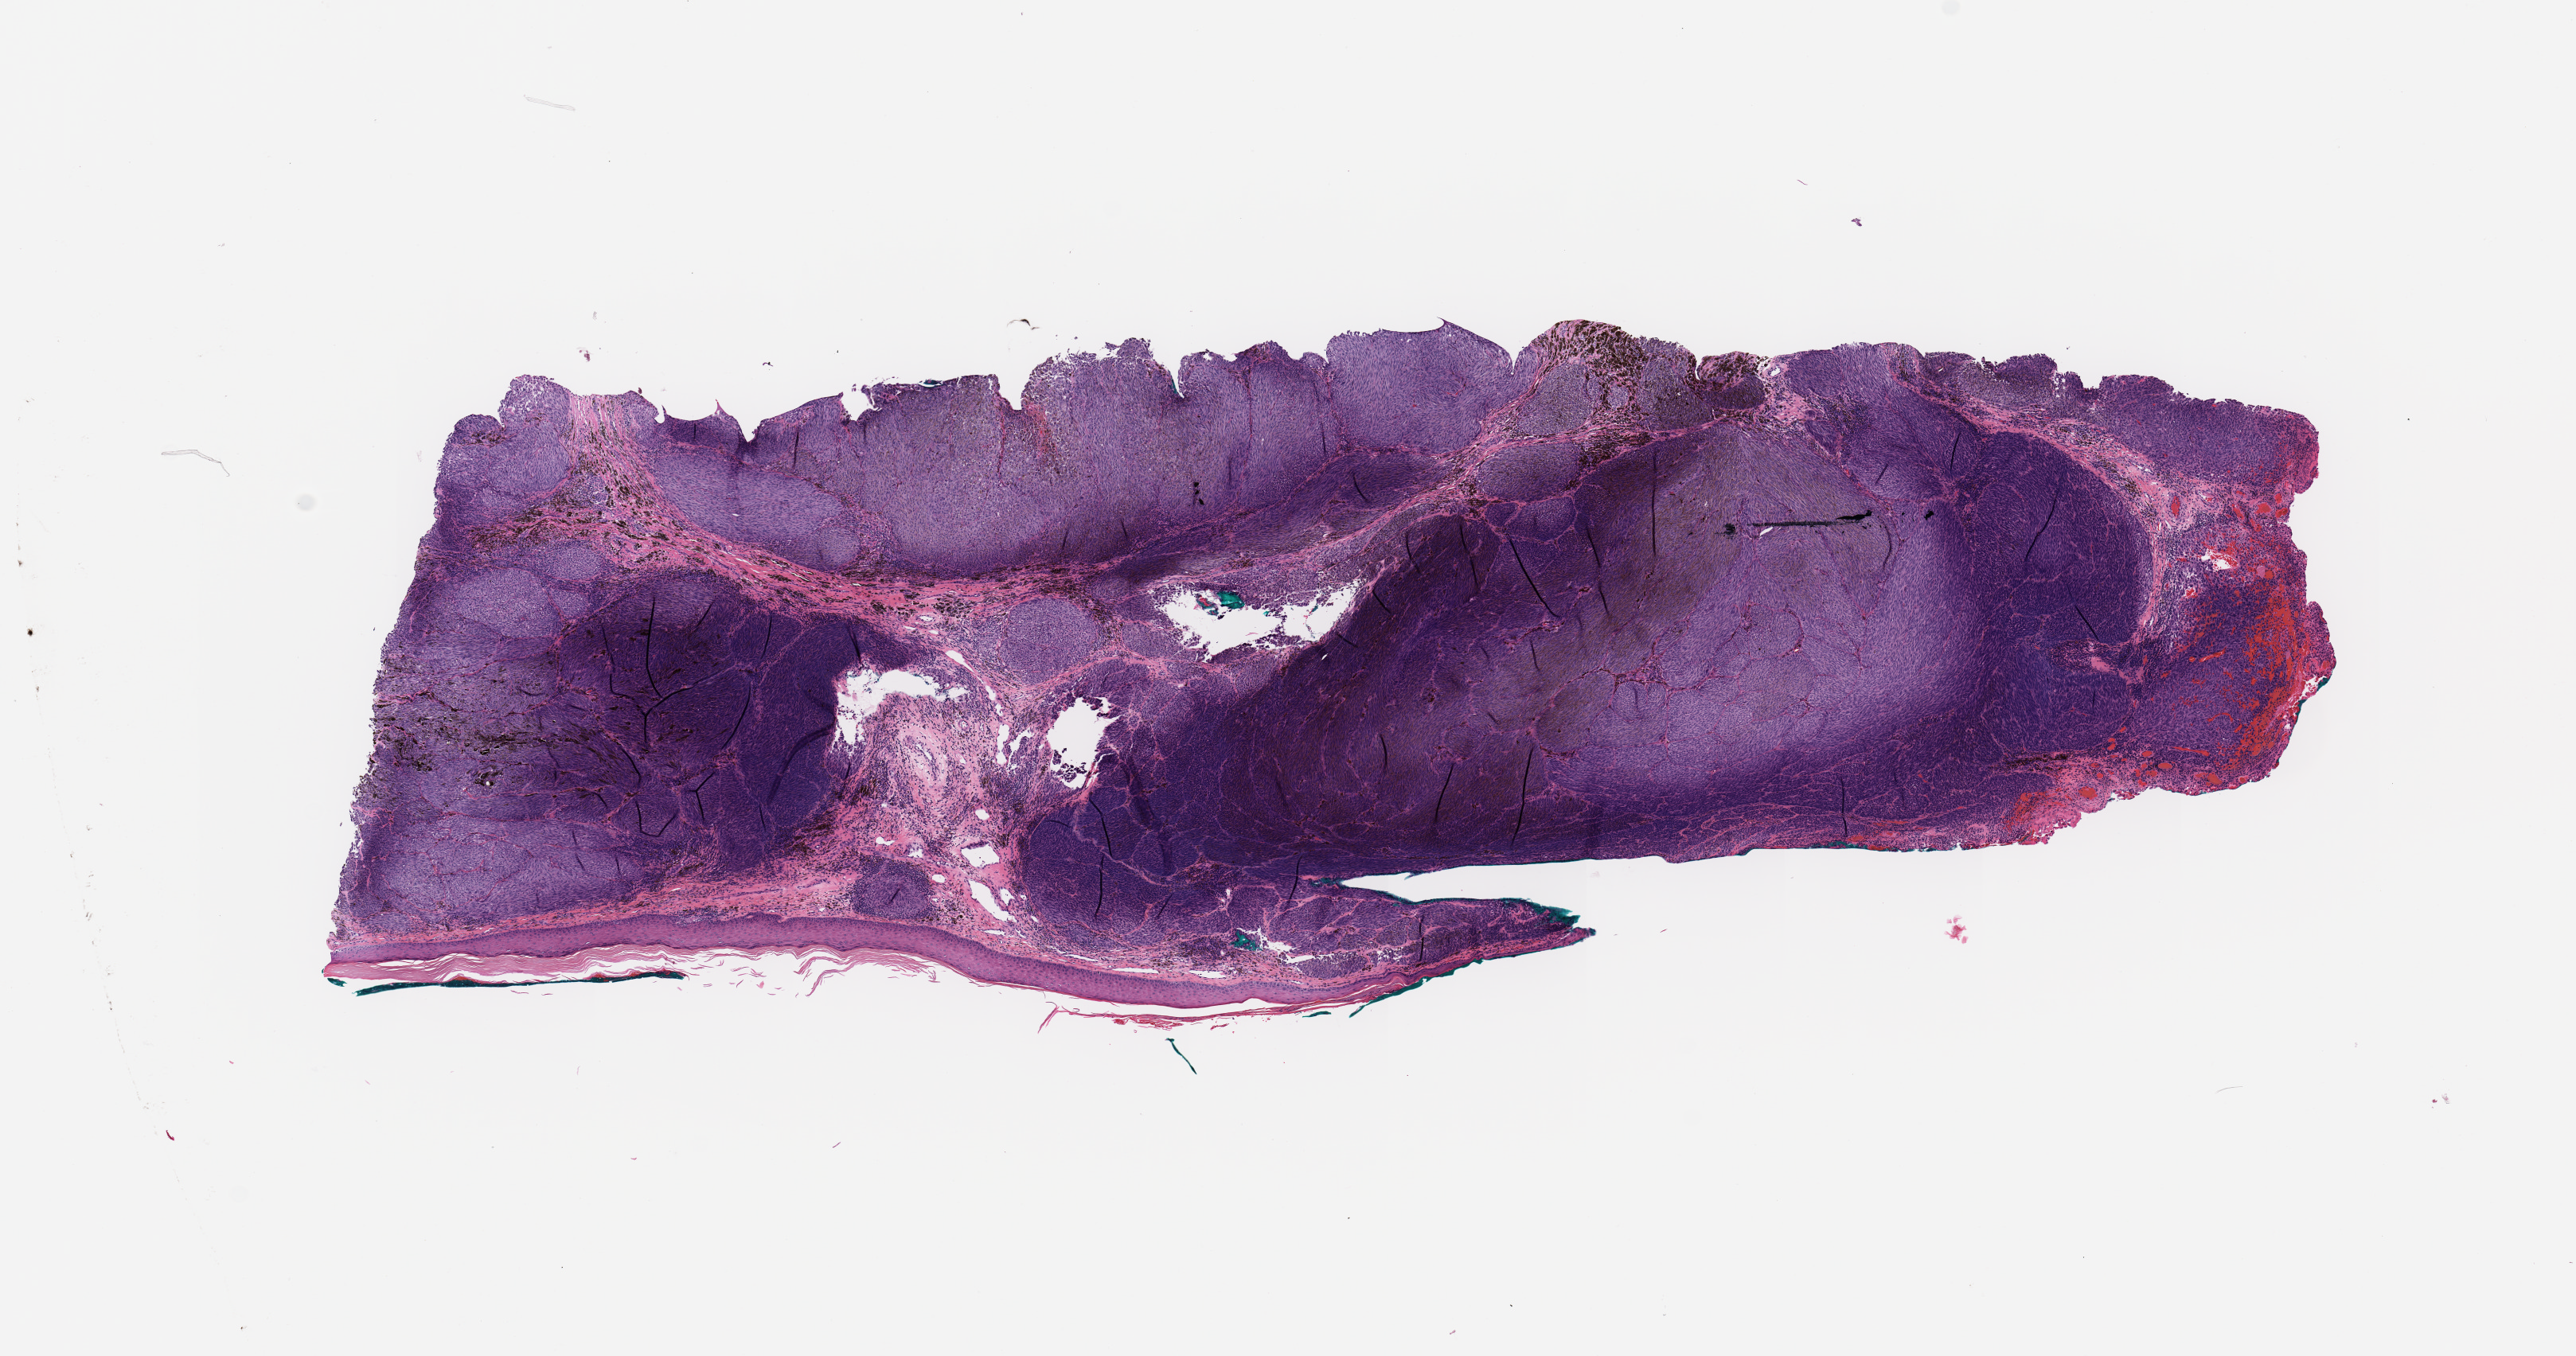
Digitized H&E-stained tissue section (whole slide), a low-resolution overview of the entire scanned area, about 12.8 x 6.7 mm (from a 20x scan), tumour tissue sample, sampled site: trunk. 78-year-old male patient. Composition of this section per pathologist review: tumour nuclei 90%, necrosis 0%.
Histologic diagnosis: Malignant melanoma, NOS. Primary tumour site (as recorded): trunk. AJCC pathologic stage: IIC.